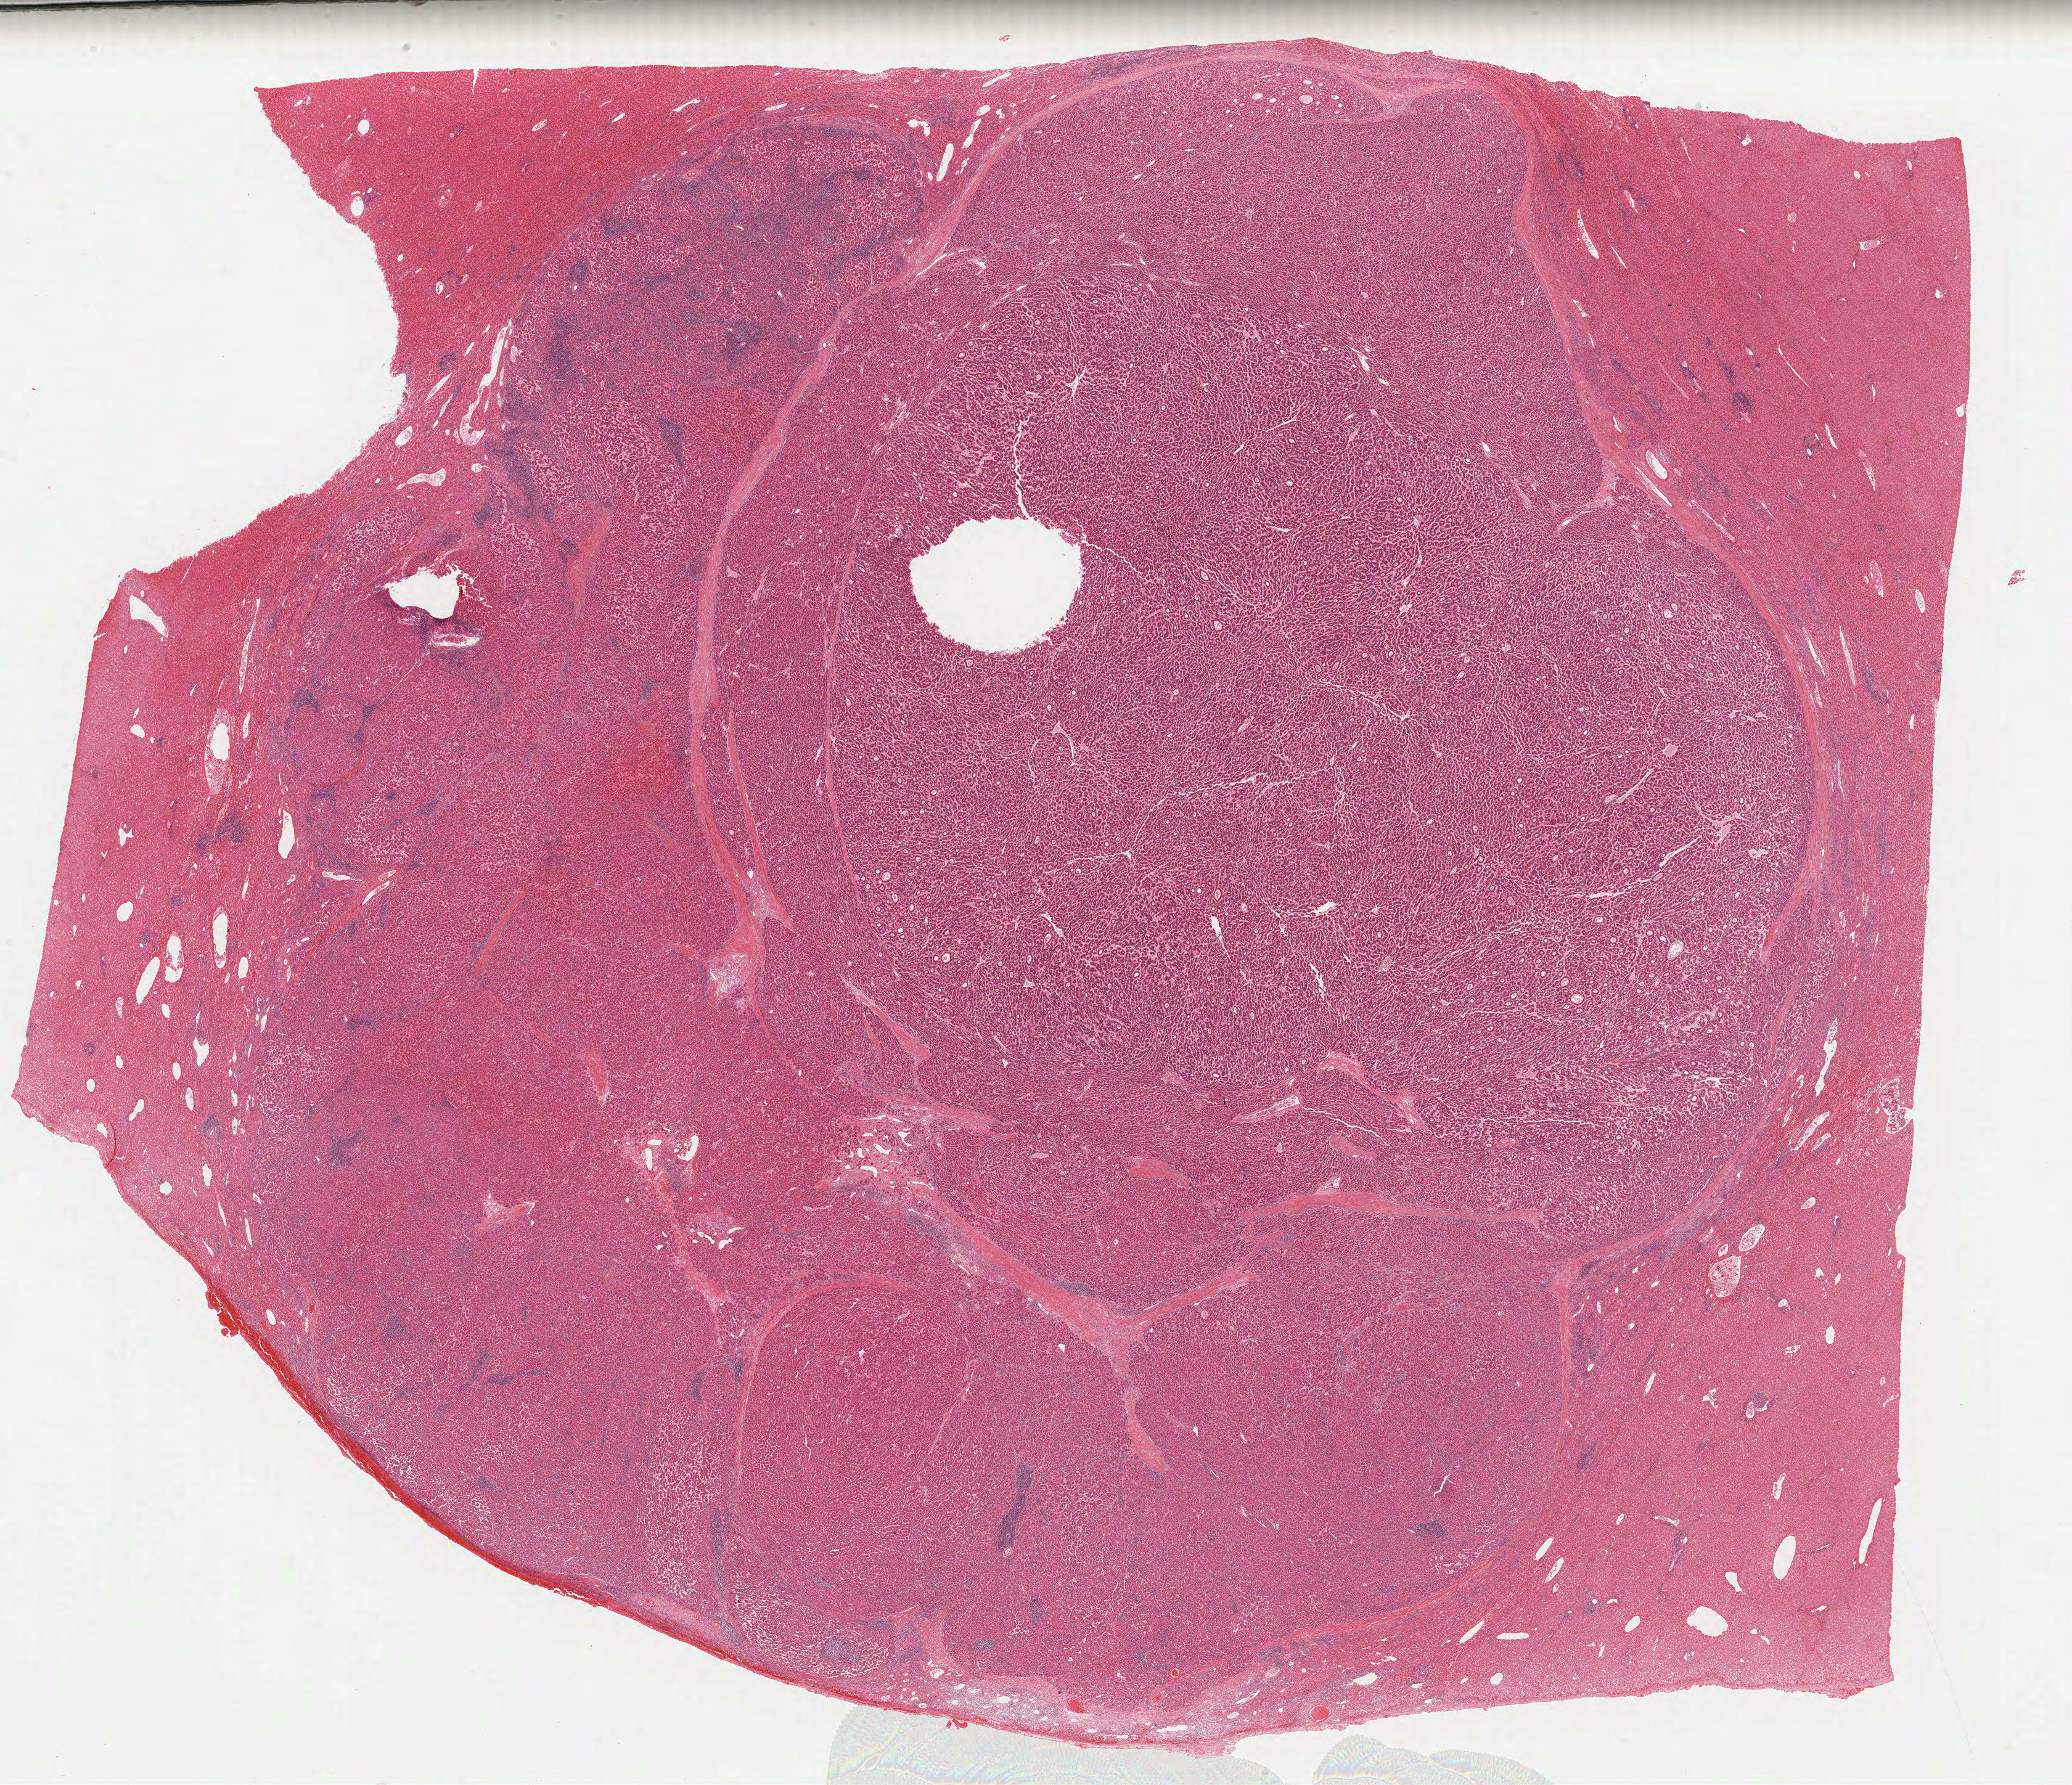
Whole-slide histology image, H&E-stained — low-resolution overview of the scanned area, about 26.6 x 22.9 mm, formalin-fixed paraffin-embedded (FFPE) diagnostic section, sample: primary tumour, liver. Male, age 69 years at initial diagnosis. Histologic grade: G2 (moderately differentiated).
* AJCC pathologic stage: I (6th edition)
* diagnosis: Hepatocellular carcinoma, NOS